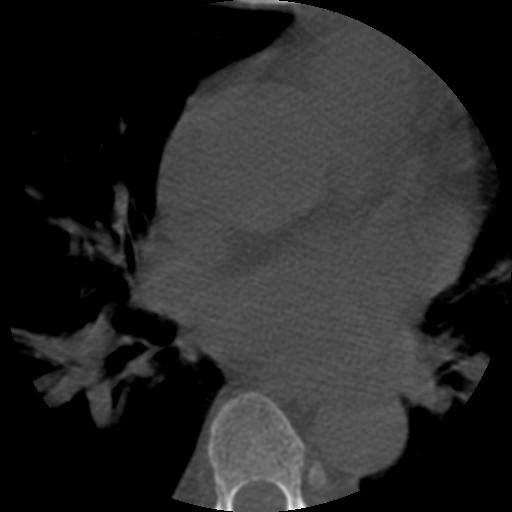
CT including the spine, one axial slice. Reconstruction kernel STANDARD. Bone window (W 1800 / L 400 HU). 1.25 mm slice thickness. 512 × 512 image matrix, field of view 160 × 160 mm. Patient age 57 years. From the clinical record (not read from this slice): primary cancer: prostate.
Annotated regions visible in this slice (semi-automatic segmentation, software-assisted and operator-edited):
- T6 vertebra: bounding box <208,392,305,512> (left, top, right, bottom; pixels)